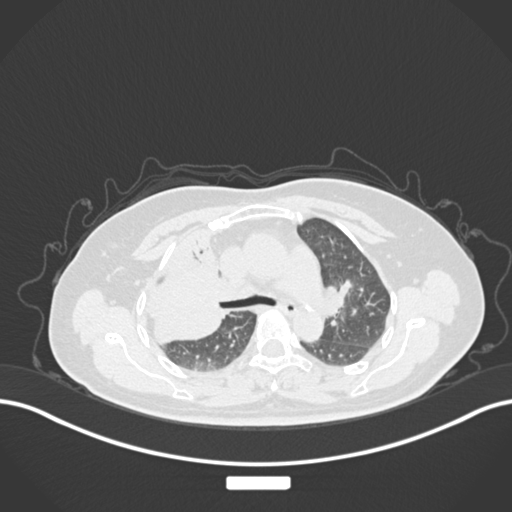
Chest CT, one axial slice. Position 103 of 177 along the scan axis. Lung window (W 1500 / L -600 HU). 1 mm slice thickness. 512 × 512 image matrix, field of view 400 × 400 mm. Patient: female, 60 years. From the clinical record (not read from this slice): clinical TNM (as recorded): T3 N1 M1.
Structures marked on this image (rectangle marked by the reading radiologist):
- lung tumour (recorded histology: adenocarcinoma): box from (x=154, y=244) to (x=229, y=352) px